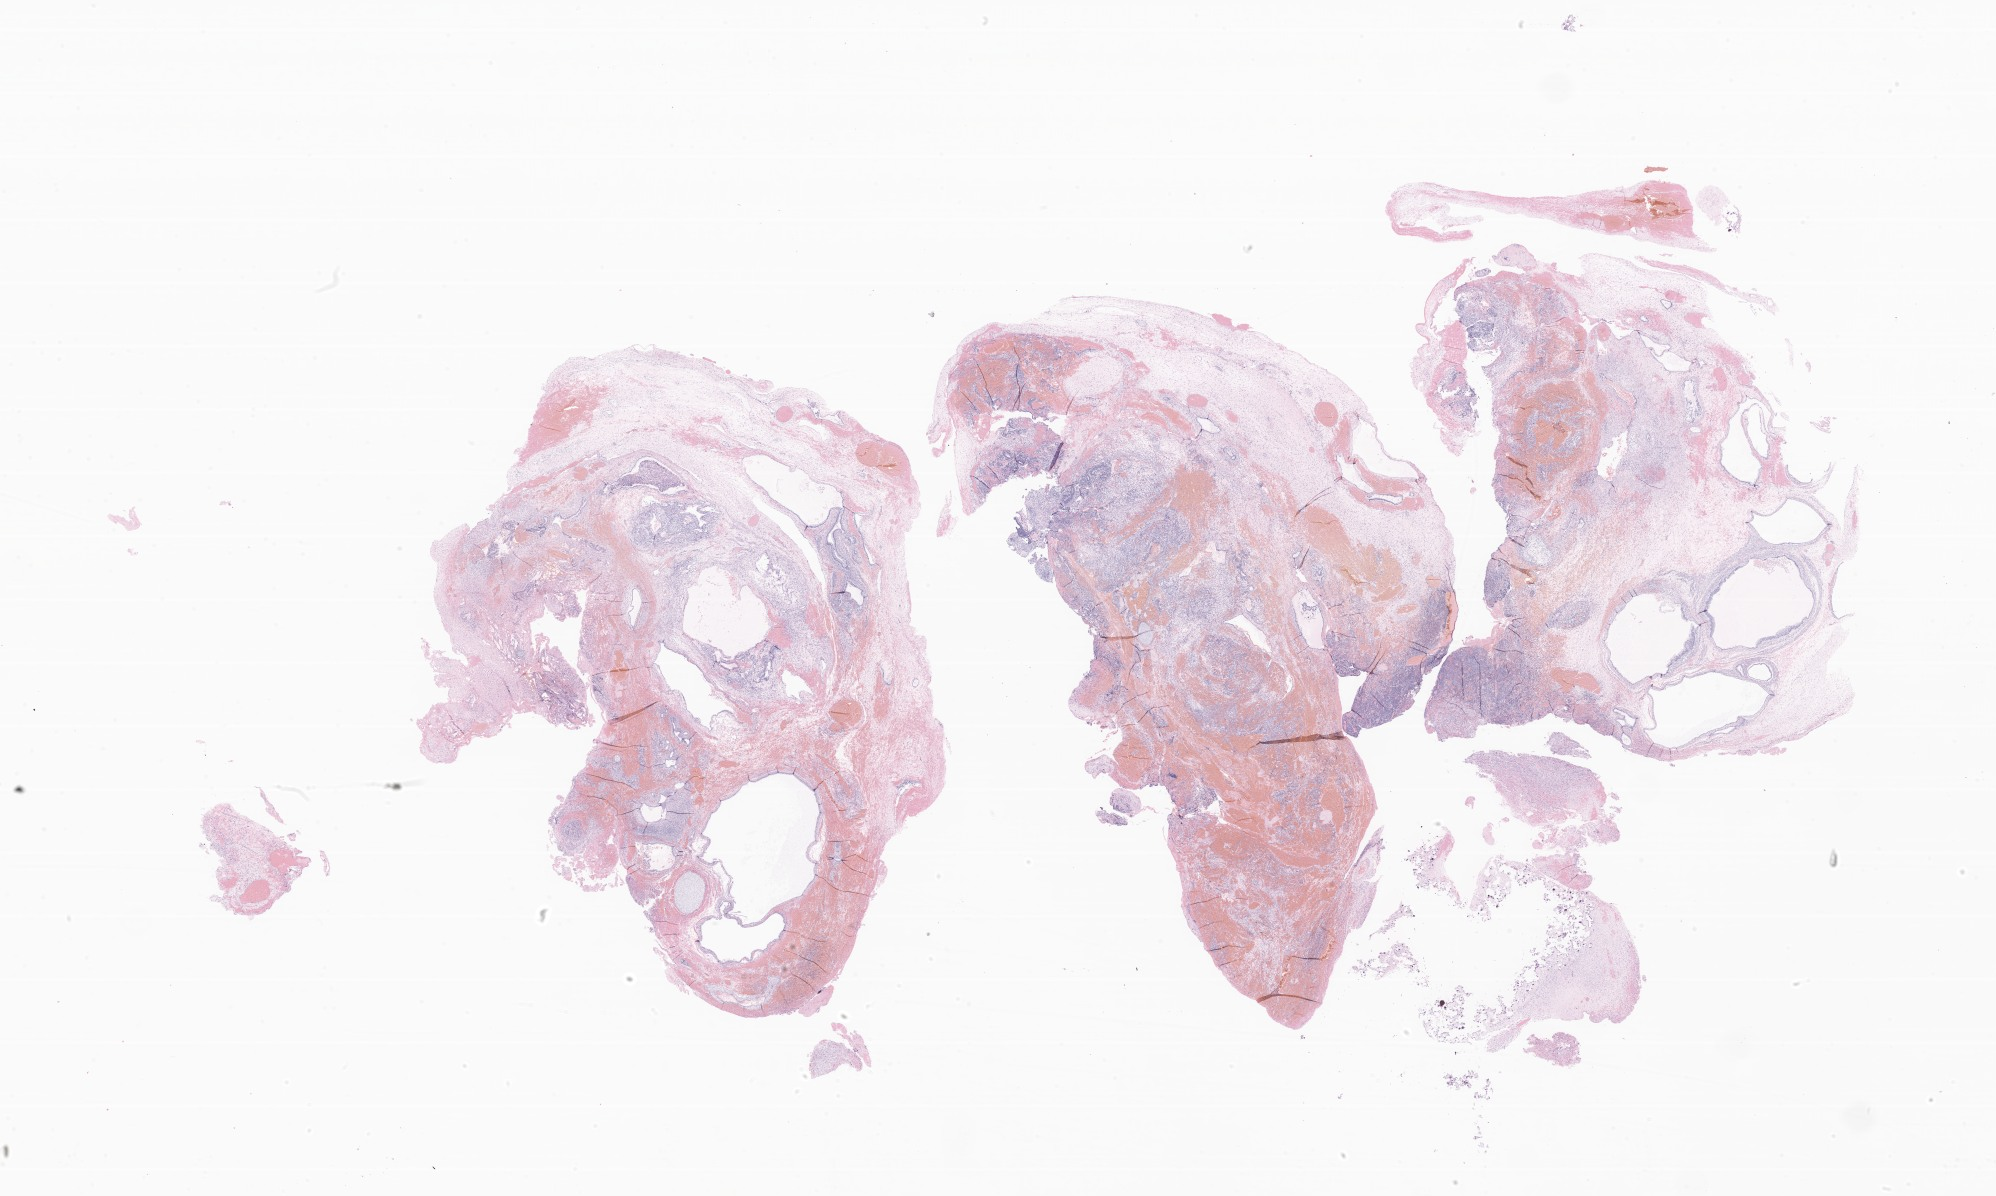
Hematoxylin and eosin (H&E) whole-slide image of tumor tissue from the pineal gland, a low-resolution overview of the entire scanned area, about 33.7 x 20.2 mm; formalin-fixed paraffin-embedded section. Patient male; age 143 months (11 years 11 months).
Diagnosis (ICD-O-3 morphology term): Teratoma, malignant, NOS.